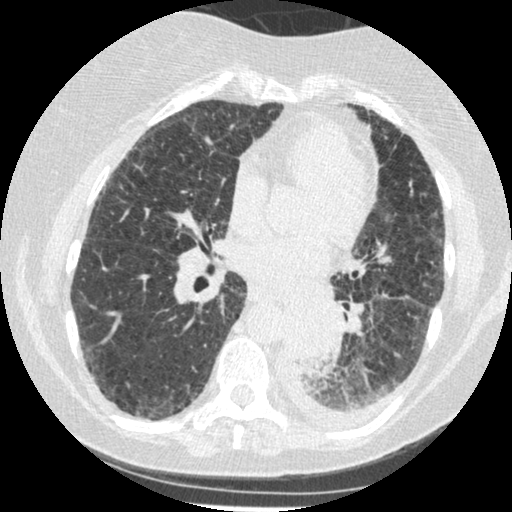
Chest CT (low-dose screening protocol), one axial image. Third annual screen. Lung window (W 1500 / L -600 HU). Female participant, aged 60 years at enrolment. Former smoker at enrolment.
Expert-annotated lung lesion, box from (x=275, y=304) to (x=343, y=376) px. Screening reader's record for this exam (one nodule recorded; not confirmed to be the boxed lesion): non-calcified nodule or mass ≥4 mm, left lower lobe, 54 × 38 mm, smooth margins, soft tissue attenuation, pre-existing on the prior screen: yes; interval growth: yes. Participant outcome: lung cancer diagnosed 15 days after this screen — small cell carcinoma, NOS, left lower lobe, undifferentiated (G4), stage IV (AJCC 6th edition), 69 mm at pathology.